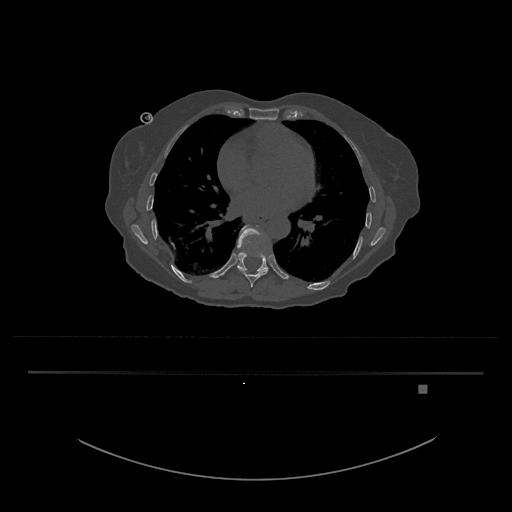
CT including the spine, one axial slice; slice 740 of 797 in the series (ordered by position); 120 kVp; bone window (W 1800 / L 400 HU); 0.5 mm slice thickness; 512 × 512 image matrix. Female patient, age 57 years. From the clinical record (not read from this slice): primary cancer: cervical.
Structures marked on this image (semi-automatically segmented with operator editing):
- T10 vertebra: bounding box <237,225,268,271> (left, top, right, bottom; pixels)
- T9 vertebra: <239,269,268,288>